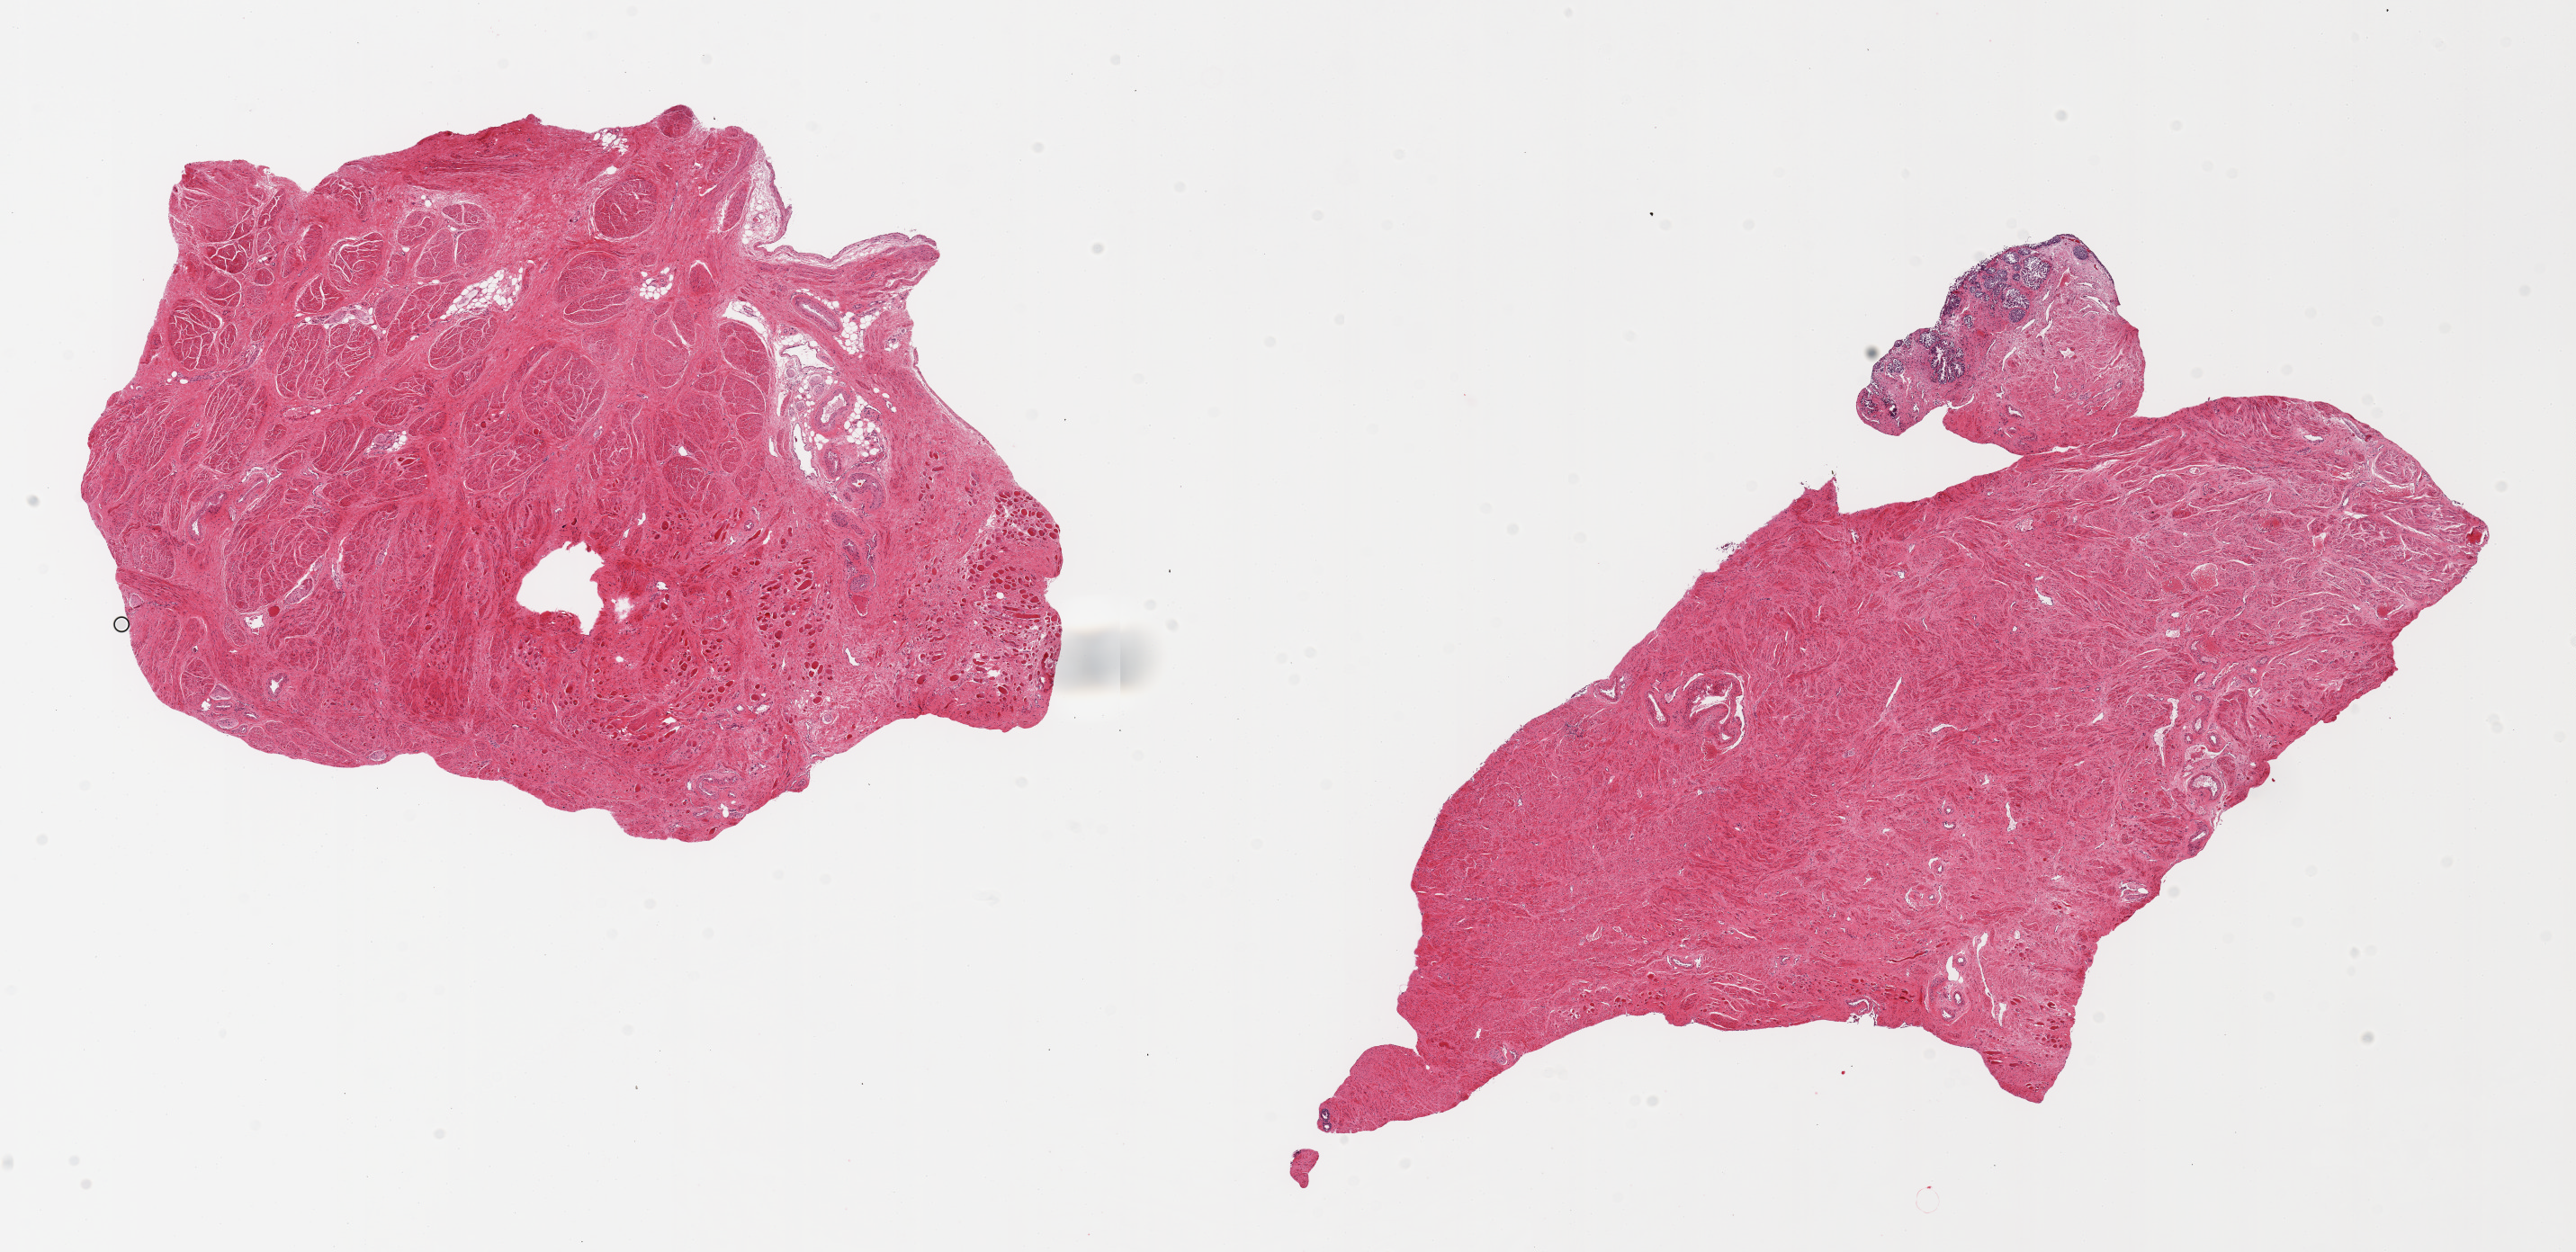
Whole-slide image, H&E stain — shown as a low-resolution overview of the whole scanned area (about 22.6 x 11.0 mm); PAXgene-fixed paraffin-embedded (PFPE) section; section of prostate (target tissue); tissue donor sample. Donor sex: male.
Reviewer comment on this tissue sample: 2 pieces; fibromuscular stroma with some skeletal muscle fibers, small portion of periurethral transitional epithelium.